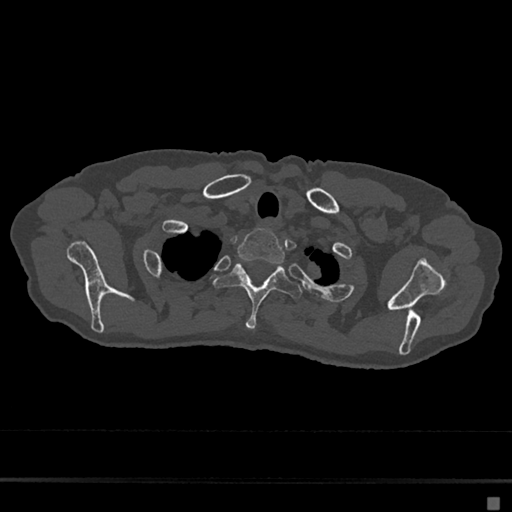
CT including the spine, one axial slice. Slice 586 of 797 in the series (ordered by position). Reconstruction kernel Br40s/3. Bone window (W 1800 / L 400 HU). 0.5 mm slice thickness. 512 × 512 image matrix, field of view 360 × 360 mm. Female patient, age 68 years. Case-level facts recorded for this patient, not image findings: primary cancer: renal.
Outlined on this slice (semi-automatic segmentation, software-assisted and operator-edited):
- T1 vertebra: box from (x=237, y=229) to (x=286, y=263) px
- T2 vertebra: (x=214, y=263)–(x=302, y=330)